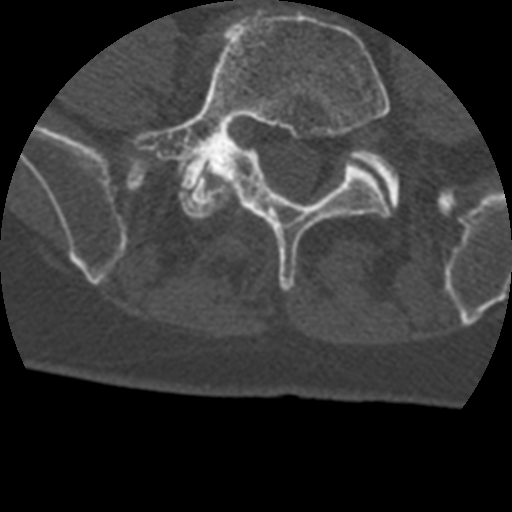
CT including the spine, one axial slice; position 42 of 399 along the scan axis; reconstruction kernel STANDARD; 120 kVp; bone window (W 1800 / L 400 HU); 1.25 mm slice thickness; 512 × 512 image matrix. Patient age 69 years. From the clinical record (not read from this slice): primary cancer: prostate.
Structures marked on this image (semi-automatic segmentation, software-assisted and operator-edited):
- L4 vertebra: bounding box (x1, y1, x2, y2) in pixels: (209, 182, 236, 211)
- L5 vertebra: (133, 11, 392, 292)